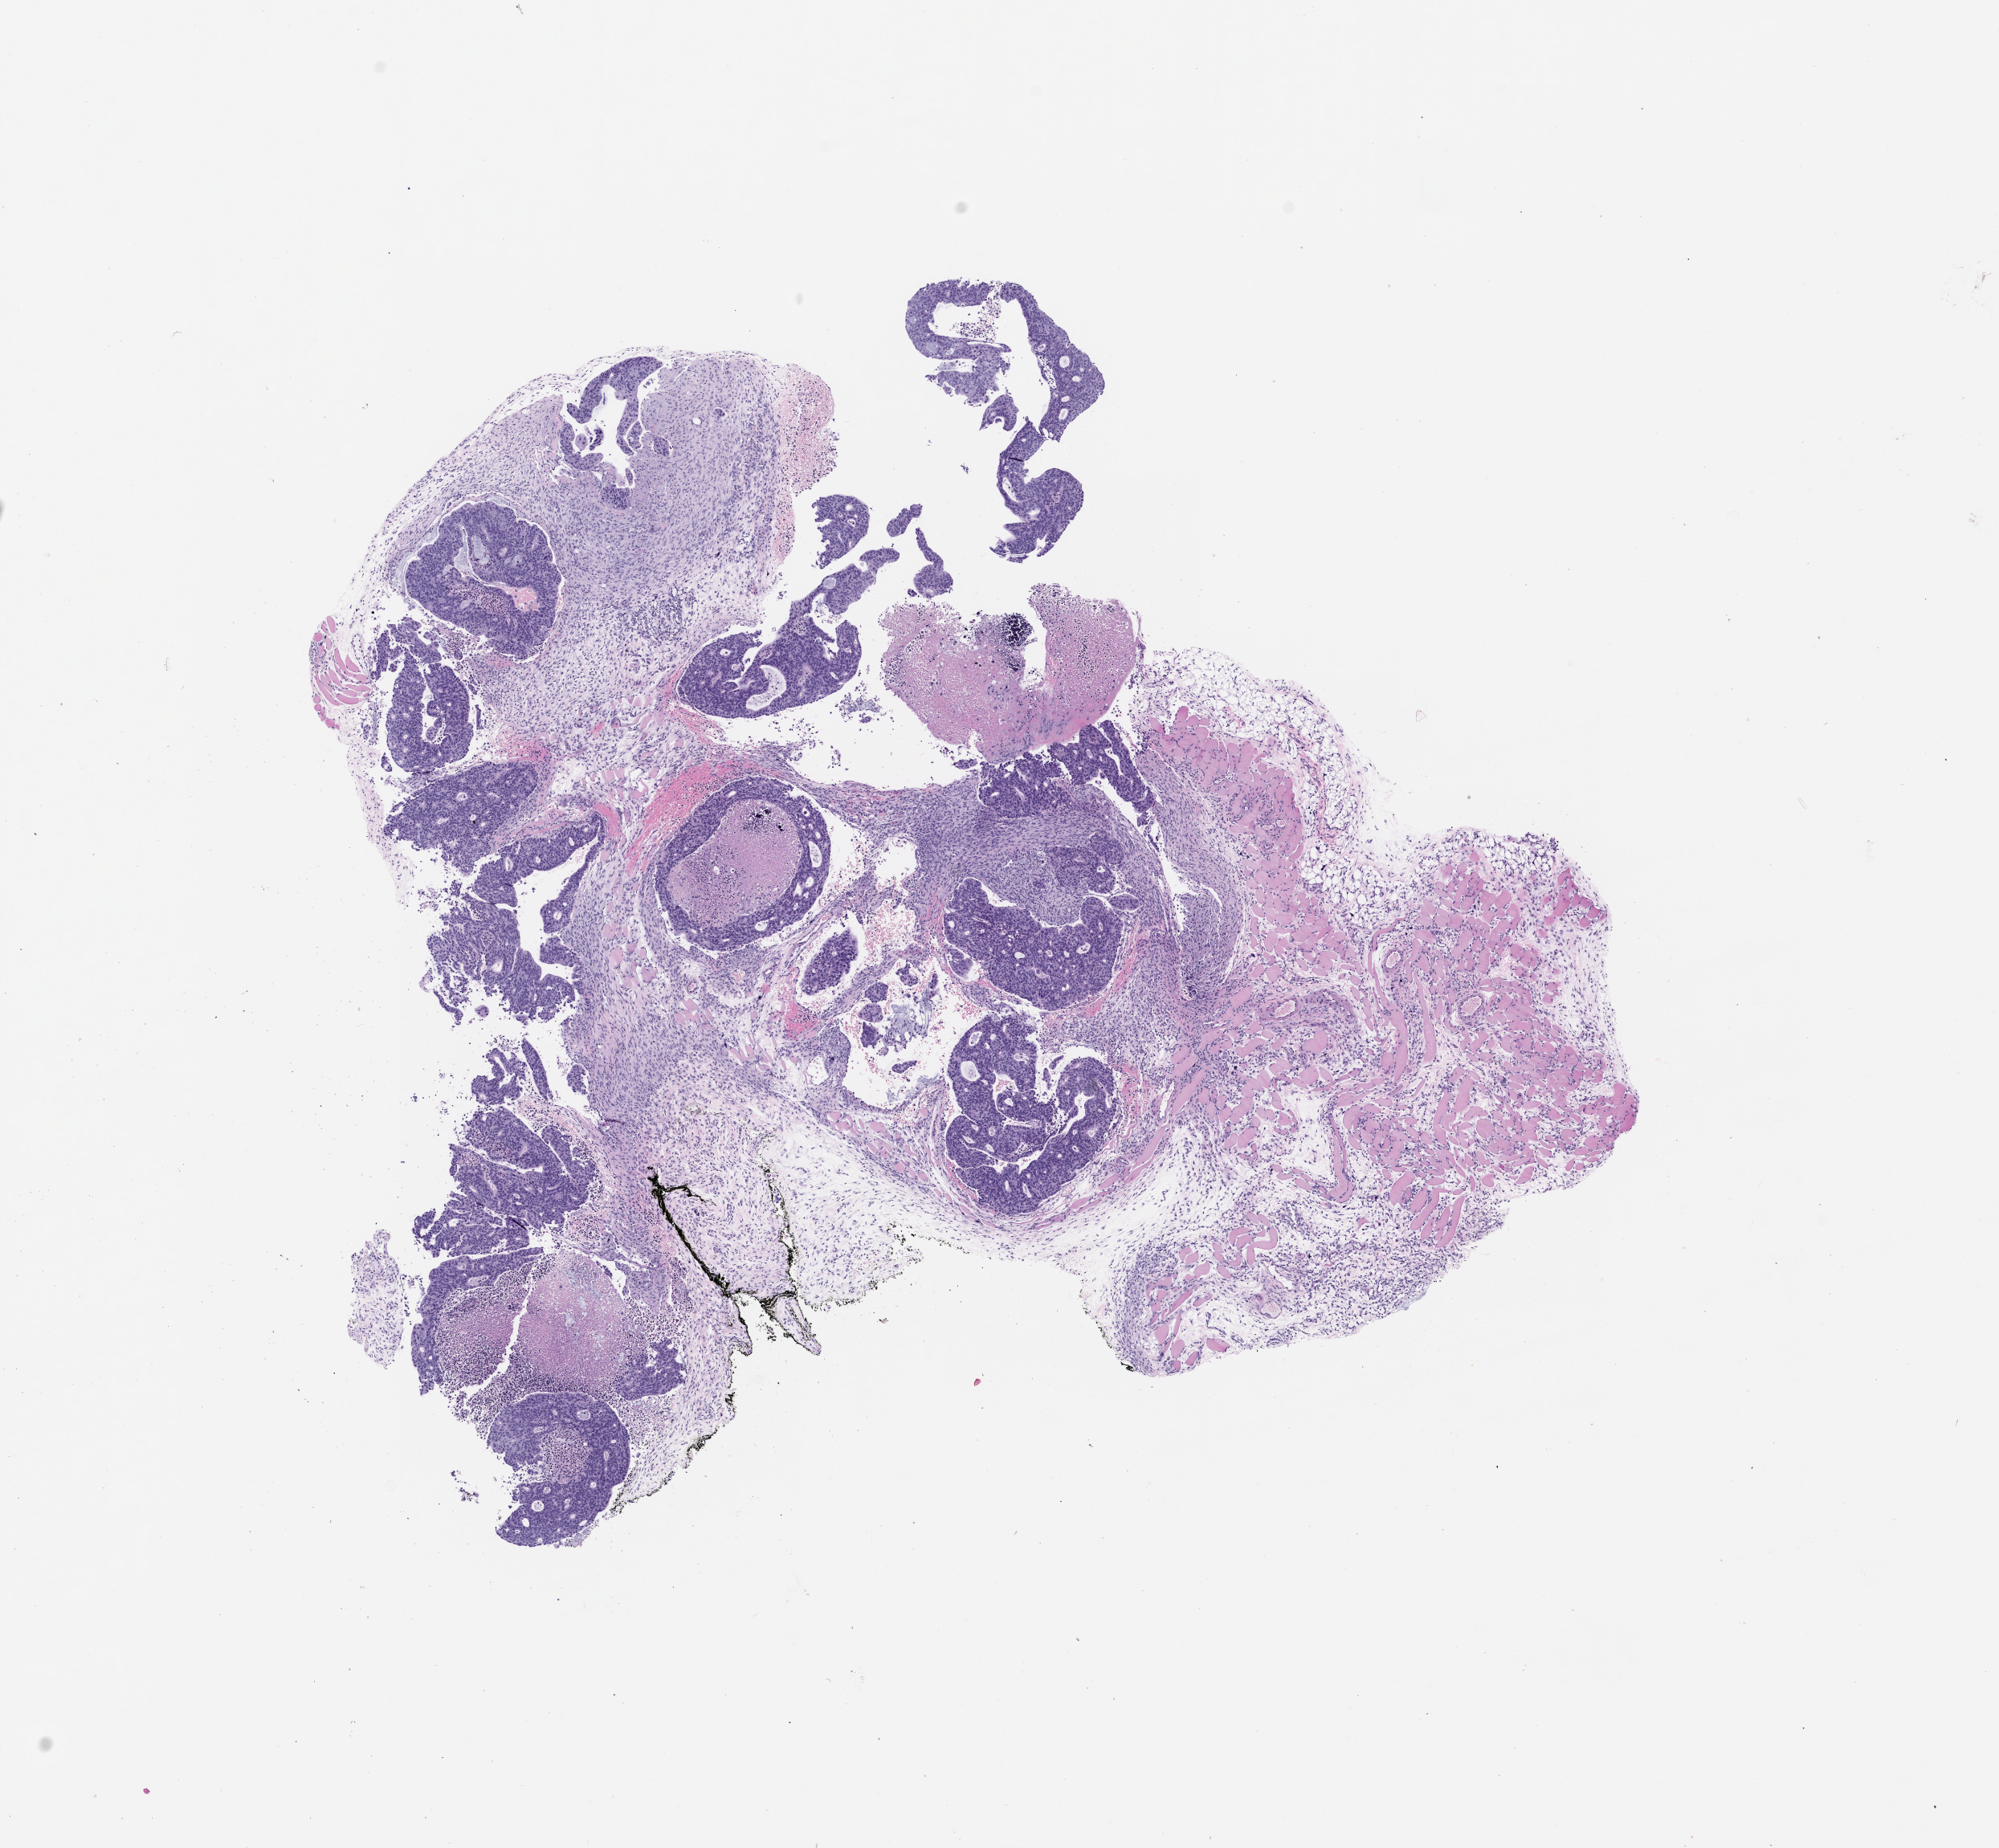
Haematoxylin and eosin whole-slide image of a patient-derived xenograft (PDX) tumor grown in a mouse, passage 0, shown as a low-resolution overview of the whole scanned area (about 10.0 x 9.2 mm). Formalin-fixed, paraffin-embedded (FFPE) tissue. Originating tumor site category: colon.
* originating patient diagnosis: Colon Adenocarcinoma